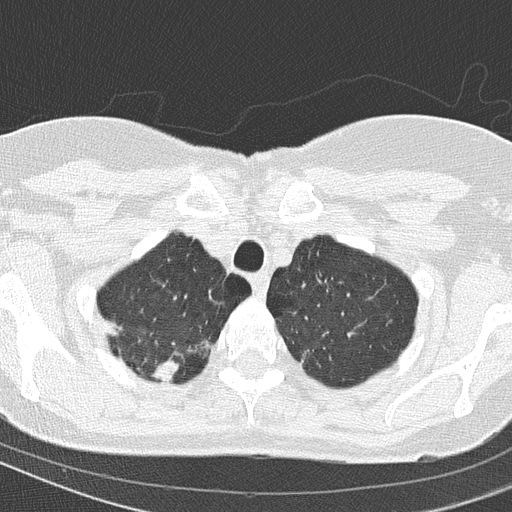
Low-dose screening chest CT, one axial slice. Position 134 of 154 along the scan axis. Lung window (W 1500 / L -600 HU). 2 mm slice thickness. 512 × 512 image matrix, field of view 288 × 288 mm.
Outlined on this slice (manually delineated by an expert):
- lesion 1 (tumor, upper lobe of right lung): box from (x=152, y=357) to (x=179, y=383) px